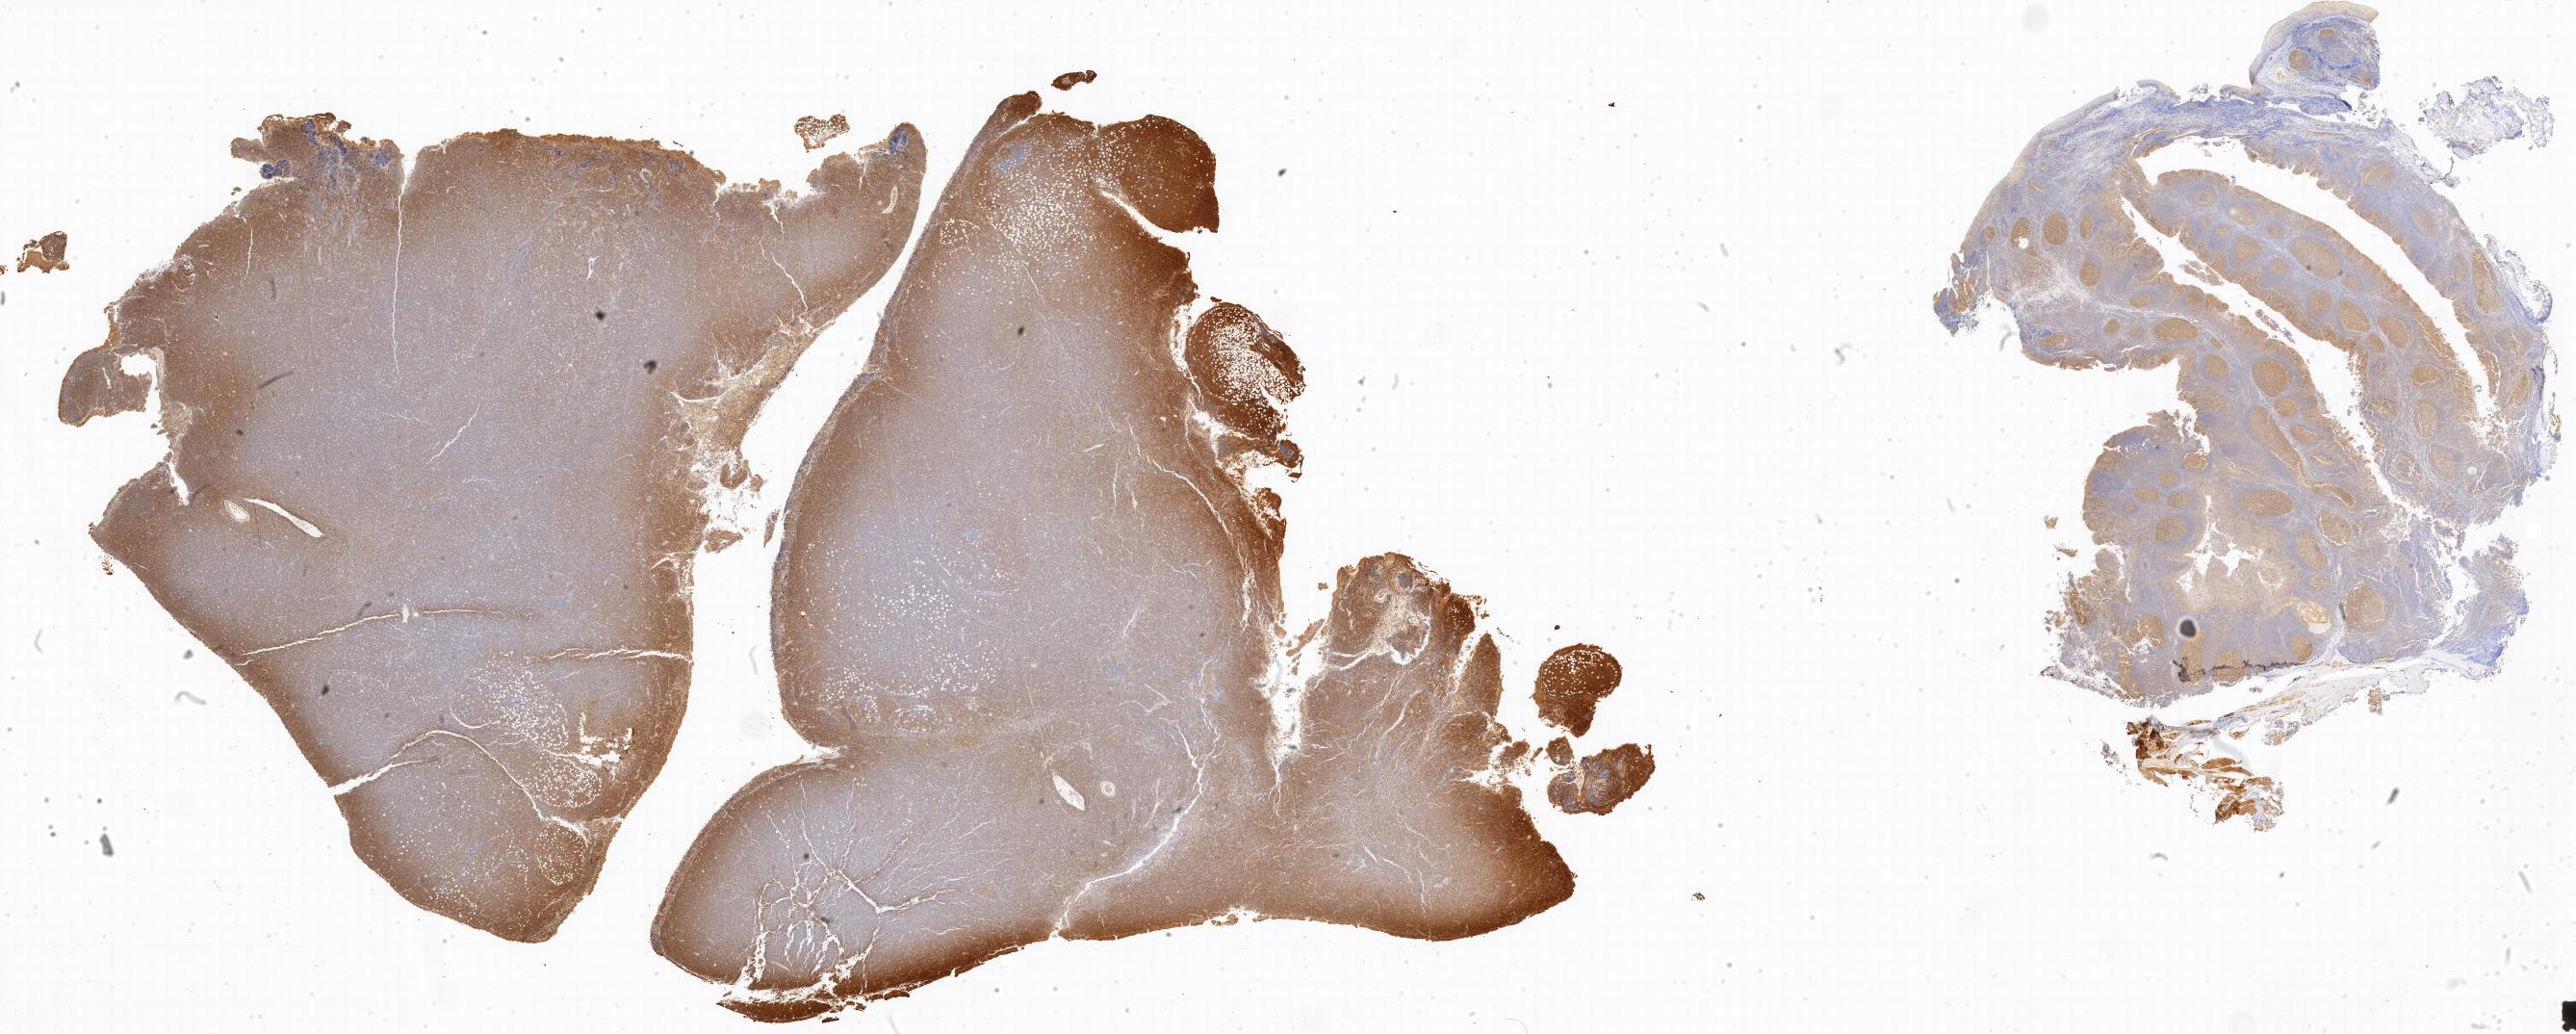
IHC for BCL6, whole-slide image, a low-resolution overview of the entire scanned area; specimen: tumor tissue; anatomic site: peritoneum. Male, age 9 years at initial diagnosis.
• diagnosis: Burkitt lymphoma, NOS